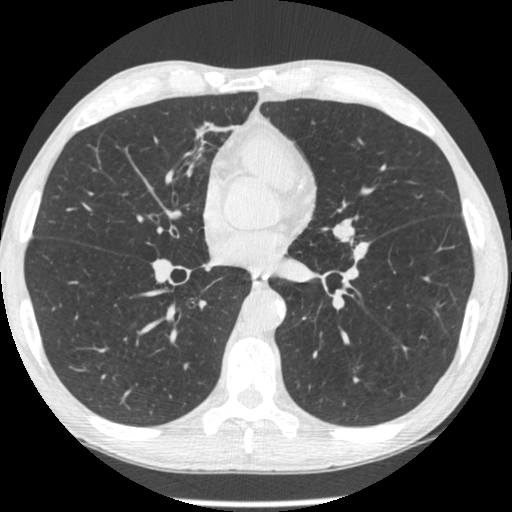
Low-dose screening chest CT, one axial slice; position 131 of 293 along the scan axis; reconstruction kernel STANDARD; lung window (W 1500 / L -600 HU); 512 × 512 image matrix, field of view 326 × 326 mm.
Outlined on this slice (expert manual segmentation):
- lesion 1 (tumor, upper lobe of left lung): box from (x=353, y=242) to (x=369, y=260) px